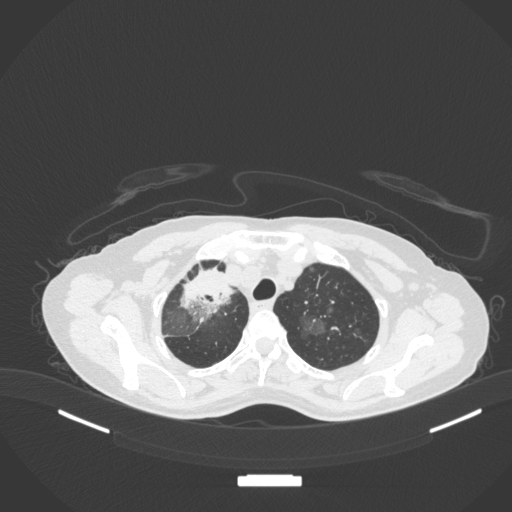
Chest CT, one axial slice; 120 kVp; lung window (W 1500 / L -600 HU); 1 mm slice thickness; 512 × 512 image matrix, field of view 400 × 400 mm. Patient: female, 59 years. From the clinical record (not read from this slice): clinical TNM (as recorded): T3 N0 M0; histopathological grade: G1.
Annotated regions visible in this slice (rectangle marked by the reading radiologist):
- lung tumour (recorded histology: adenocarcinoma): box from (x=181, y=259) to (x=235, y=319) px